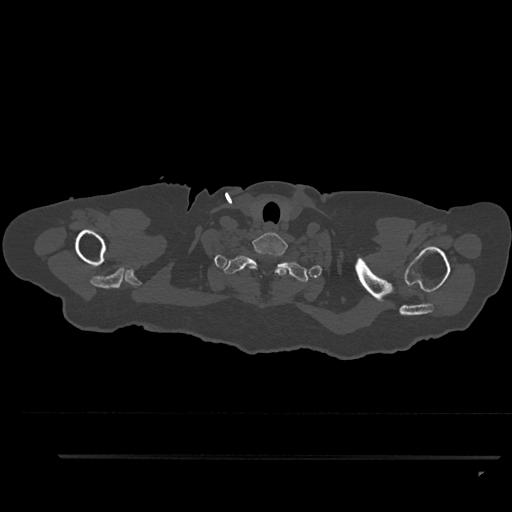
CT including the spine, one axial slice. Position 777 of 797 along the scan axis. Reconstruction kernel Br40s/3. Bone window (W 1800 / L 400 HU). 0.5 mm slice thickness. 512 × 512 image matrix, field of view 408 × 408 mm. Patient: female, 44 years. Case-level facts recorded for this patient, not image findings: primary cancer: renal; vertebrae with lytic lesions (as recorded): L1.
Outlined on this slice (semi-automatically segmented with operator editing):
- T1 vertebra: bounding box [x1, y1, x2, y2] px = [223, 255, 309, 282]